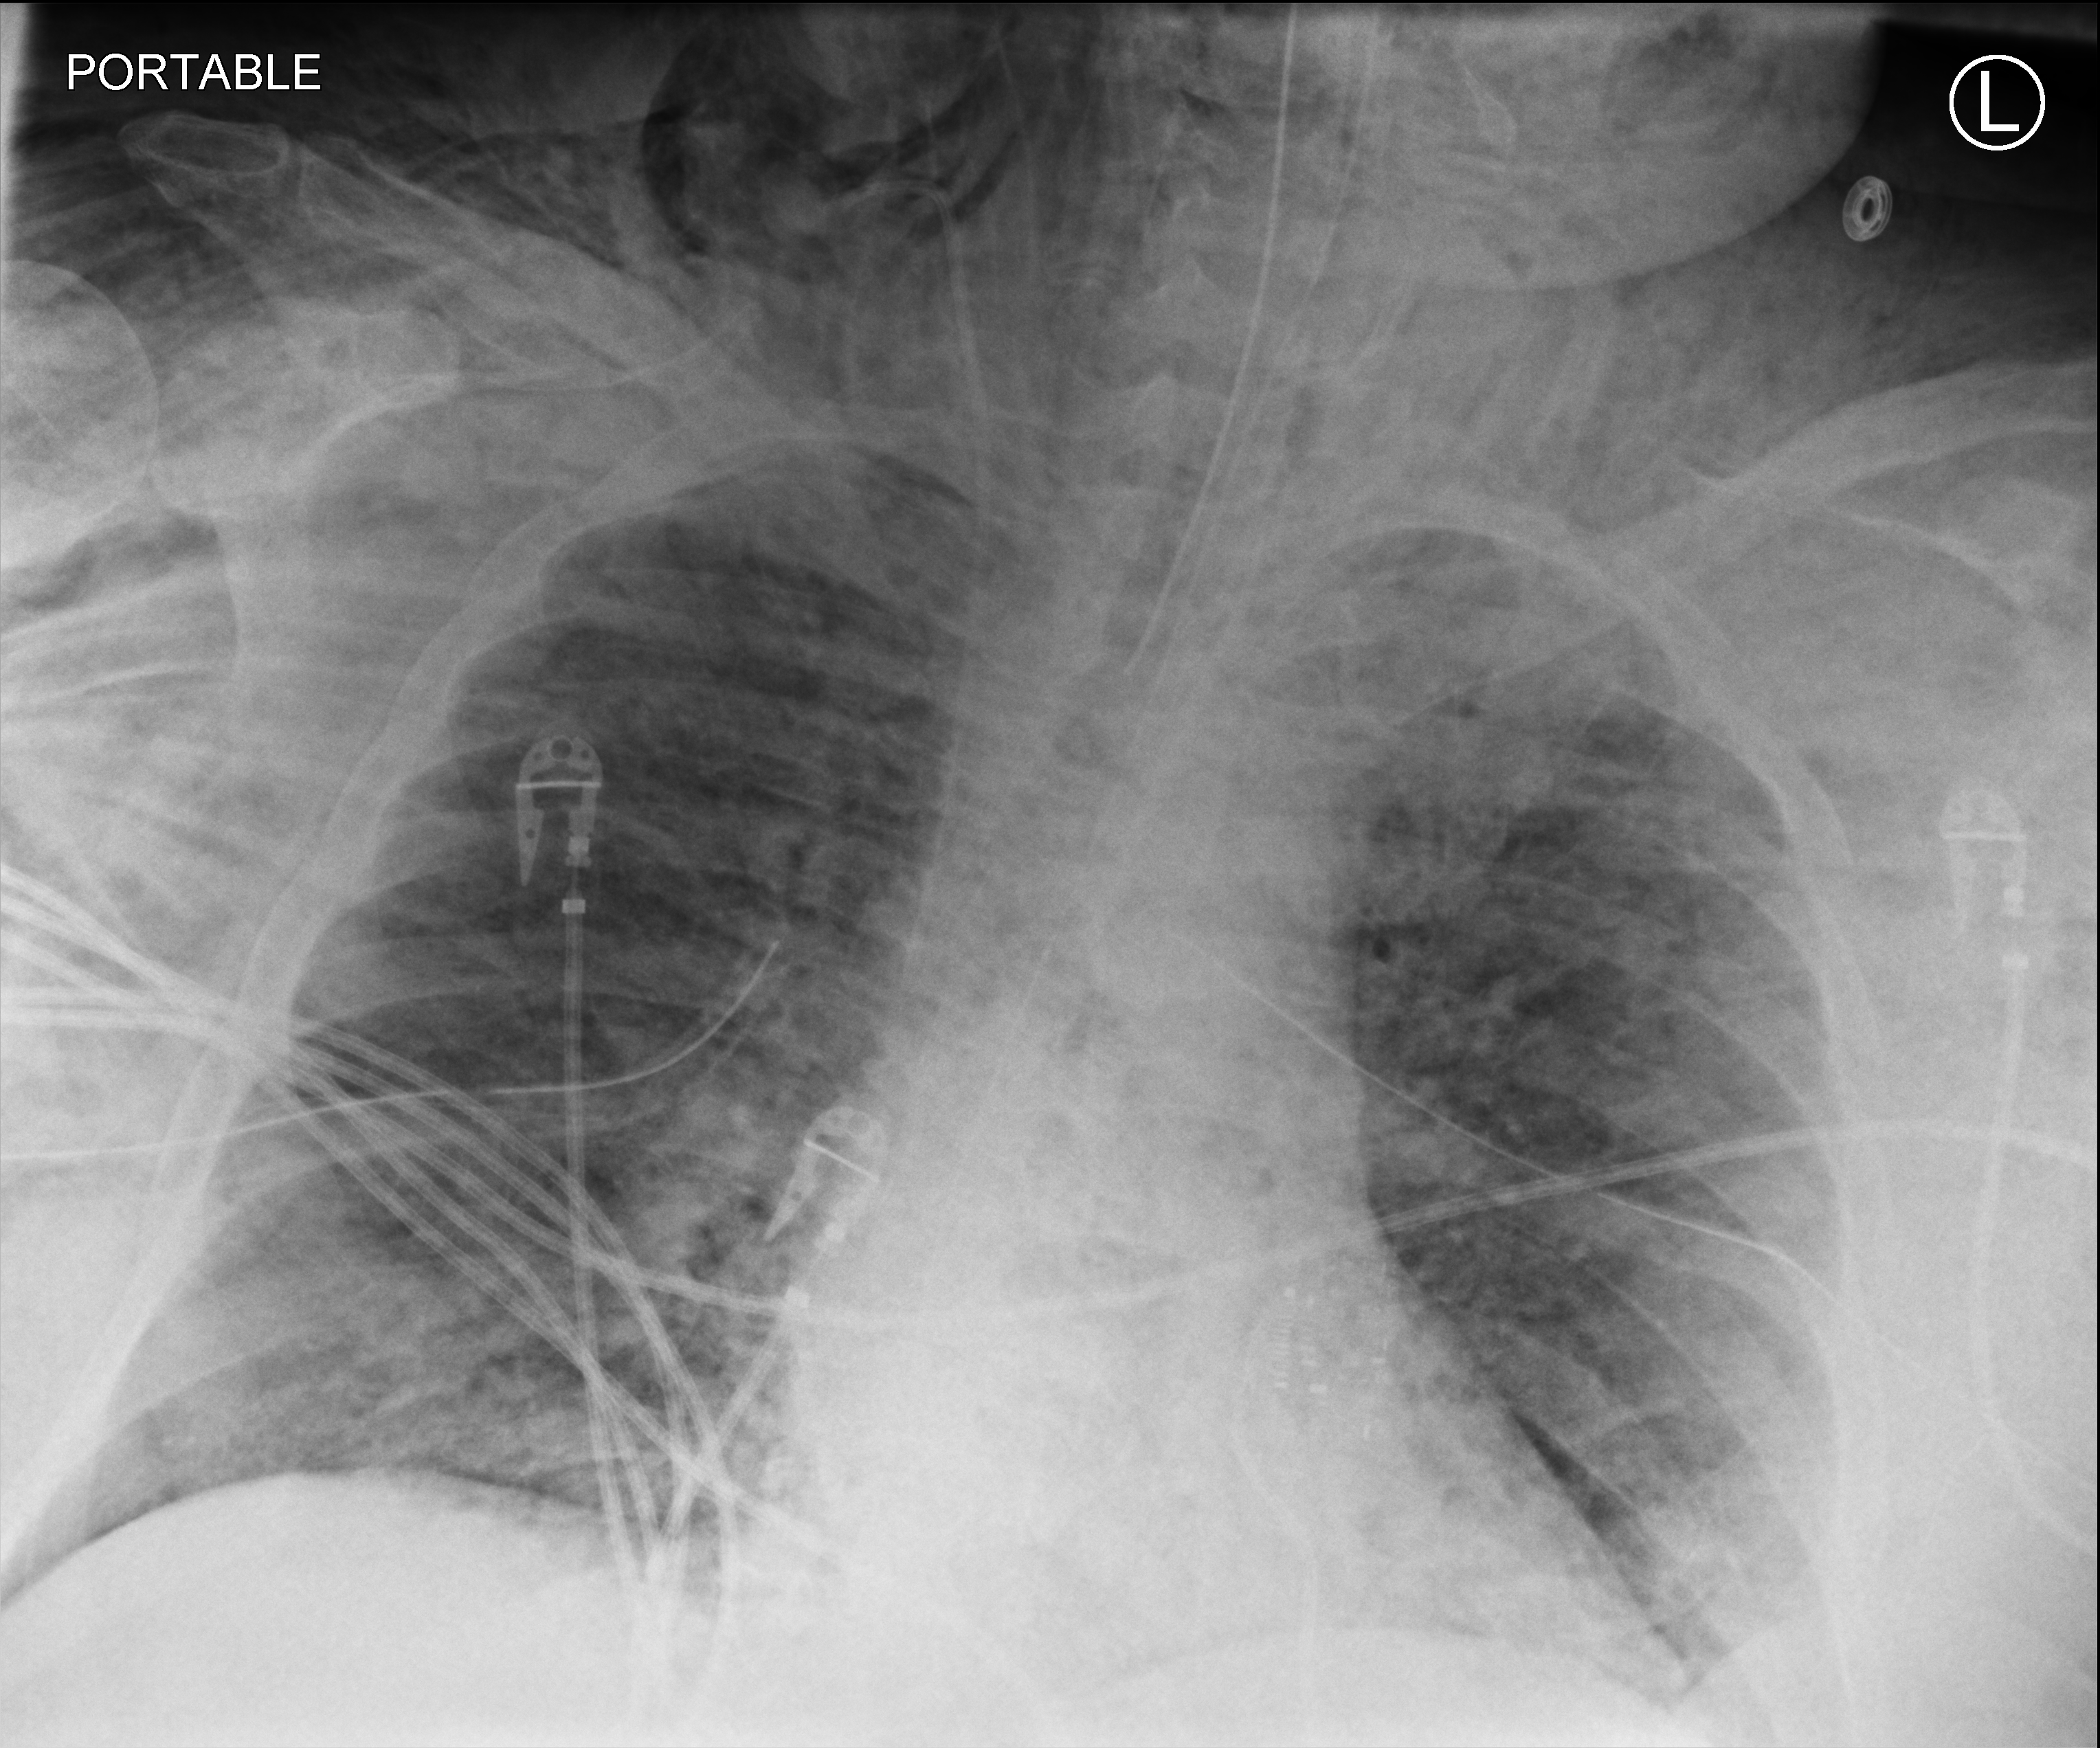
Chest X-ray (portable), anteroposterior (AP) projection. Adult patient hospitalised with COVID-19, age 18–59 years.
Admission-level facts for this patient (not findings on this image; timing relative to this image not recorded):
- mechanically ventilated during this hospital stay: yes
- admitted to intensive care during this hospital stay: yes
- other chronic lung disease (admission record): no